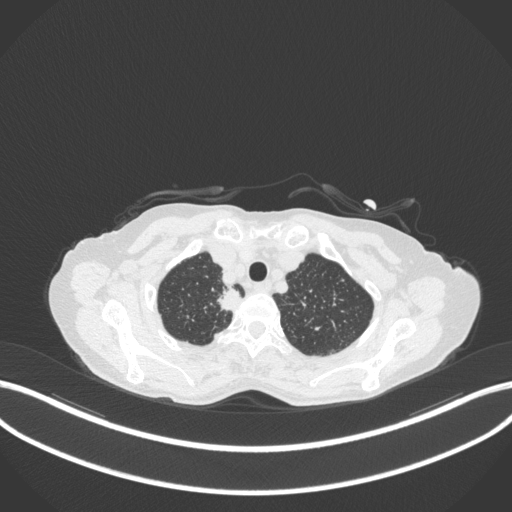
Chest CT, one axial slice. Slice 326 of 363 in the series (ordered by position). Reconstruction kernel B31f. 120 kVp. Lung window (W 1500 / L -600 HU). 1 mm slice thickness. 512 × 512 image matrix, field of view 400 × 400 mm. Female patient, age 75 years. From the clinical record (not read from this slice): clinical TNM (as recorded): T1c N1 M1.
Outlined on this slice (bounding box drawn by a radiologist):
- lung tumour (recorded histology: adenocarcinoma): bounding box [x1, y1, x2, y2] px = [209, 286, 244, 316]